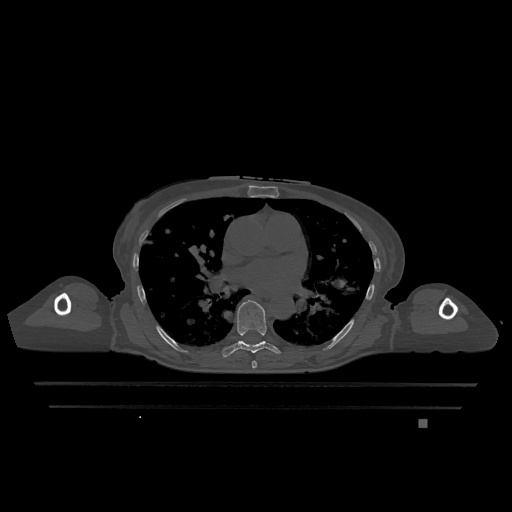
CT including the spine, one axial slice. Slice 740 of 1317 in the series (ordered by position). Bone window (W 1800 / L 400 HU). 0.5 mm slice thickness. 512 × 512 image matrix, field of view 500 × 500 mm. Patient: female, 74 years. Case-level facts recorded for this patient, not image findings: primary cancer: lung.
Outlined on this slice (semi-automatically segmented with operator editing):
- T6 vertebra: bounding box <252,361,257,369> (left, top, right, bottom; pixels)
- T7 vertebra: <222,300,280,358>